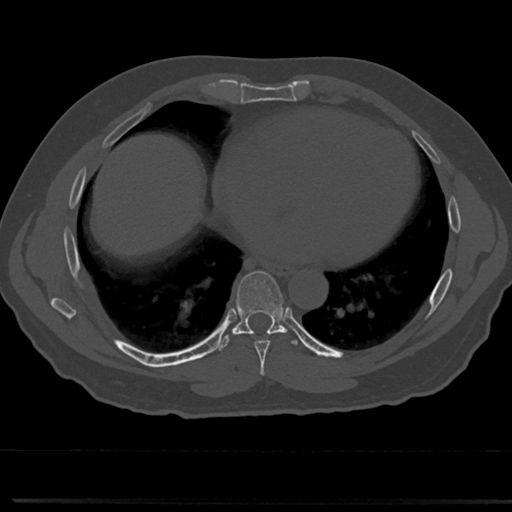
CT including the spine, one axial slice. Position 374 of 817 along the scan axis. Bone window (W 1800 / L 400 HU). 512 × 512 image matrix, field of view 355 × 355 mm. Patient: male, 61 years. Case-level facts recorded for this patient, not image findings: primary cancer: prostate.
Structures marked on this image (semi-automatically segmented with operator editing):
- T7 vertebra: bounding box [x1, y1, x2, y2] px = [234, 272, 289, 356]
- T8 vertebra: [238, 326, 281, 333]